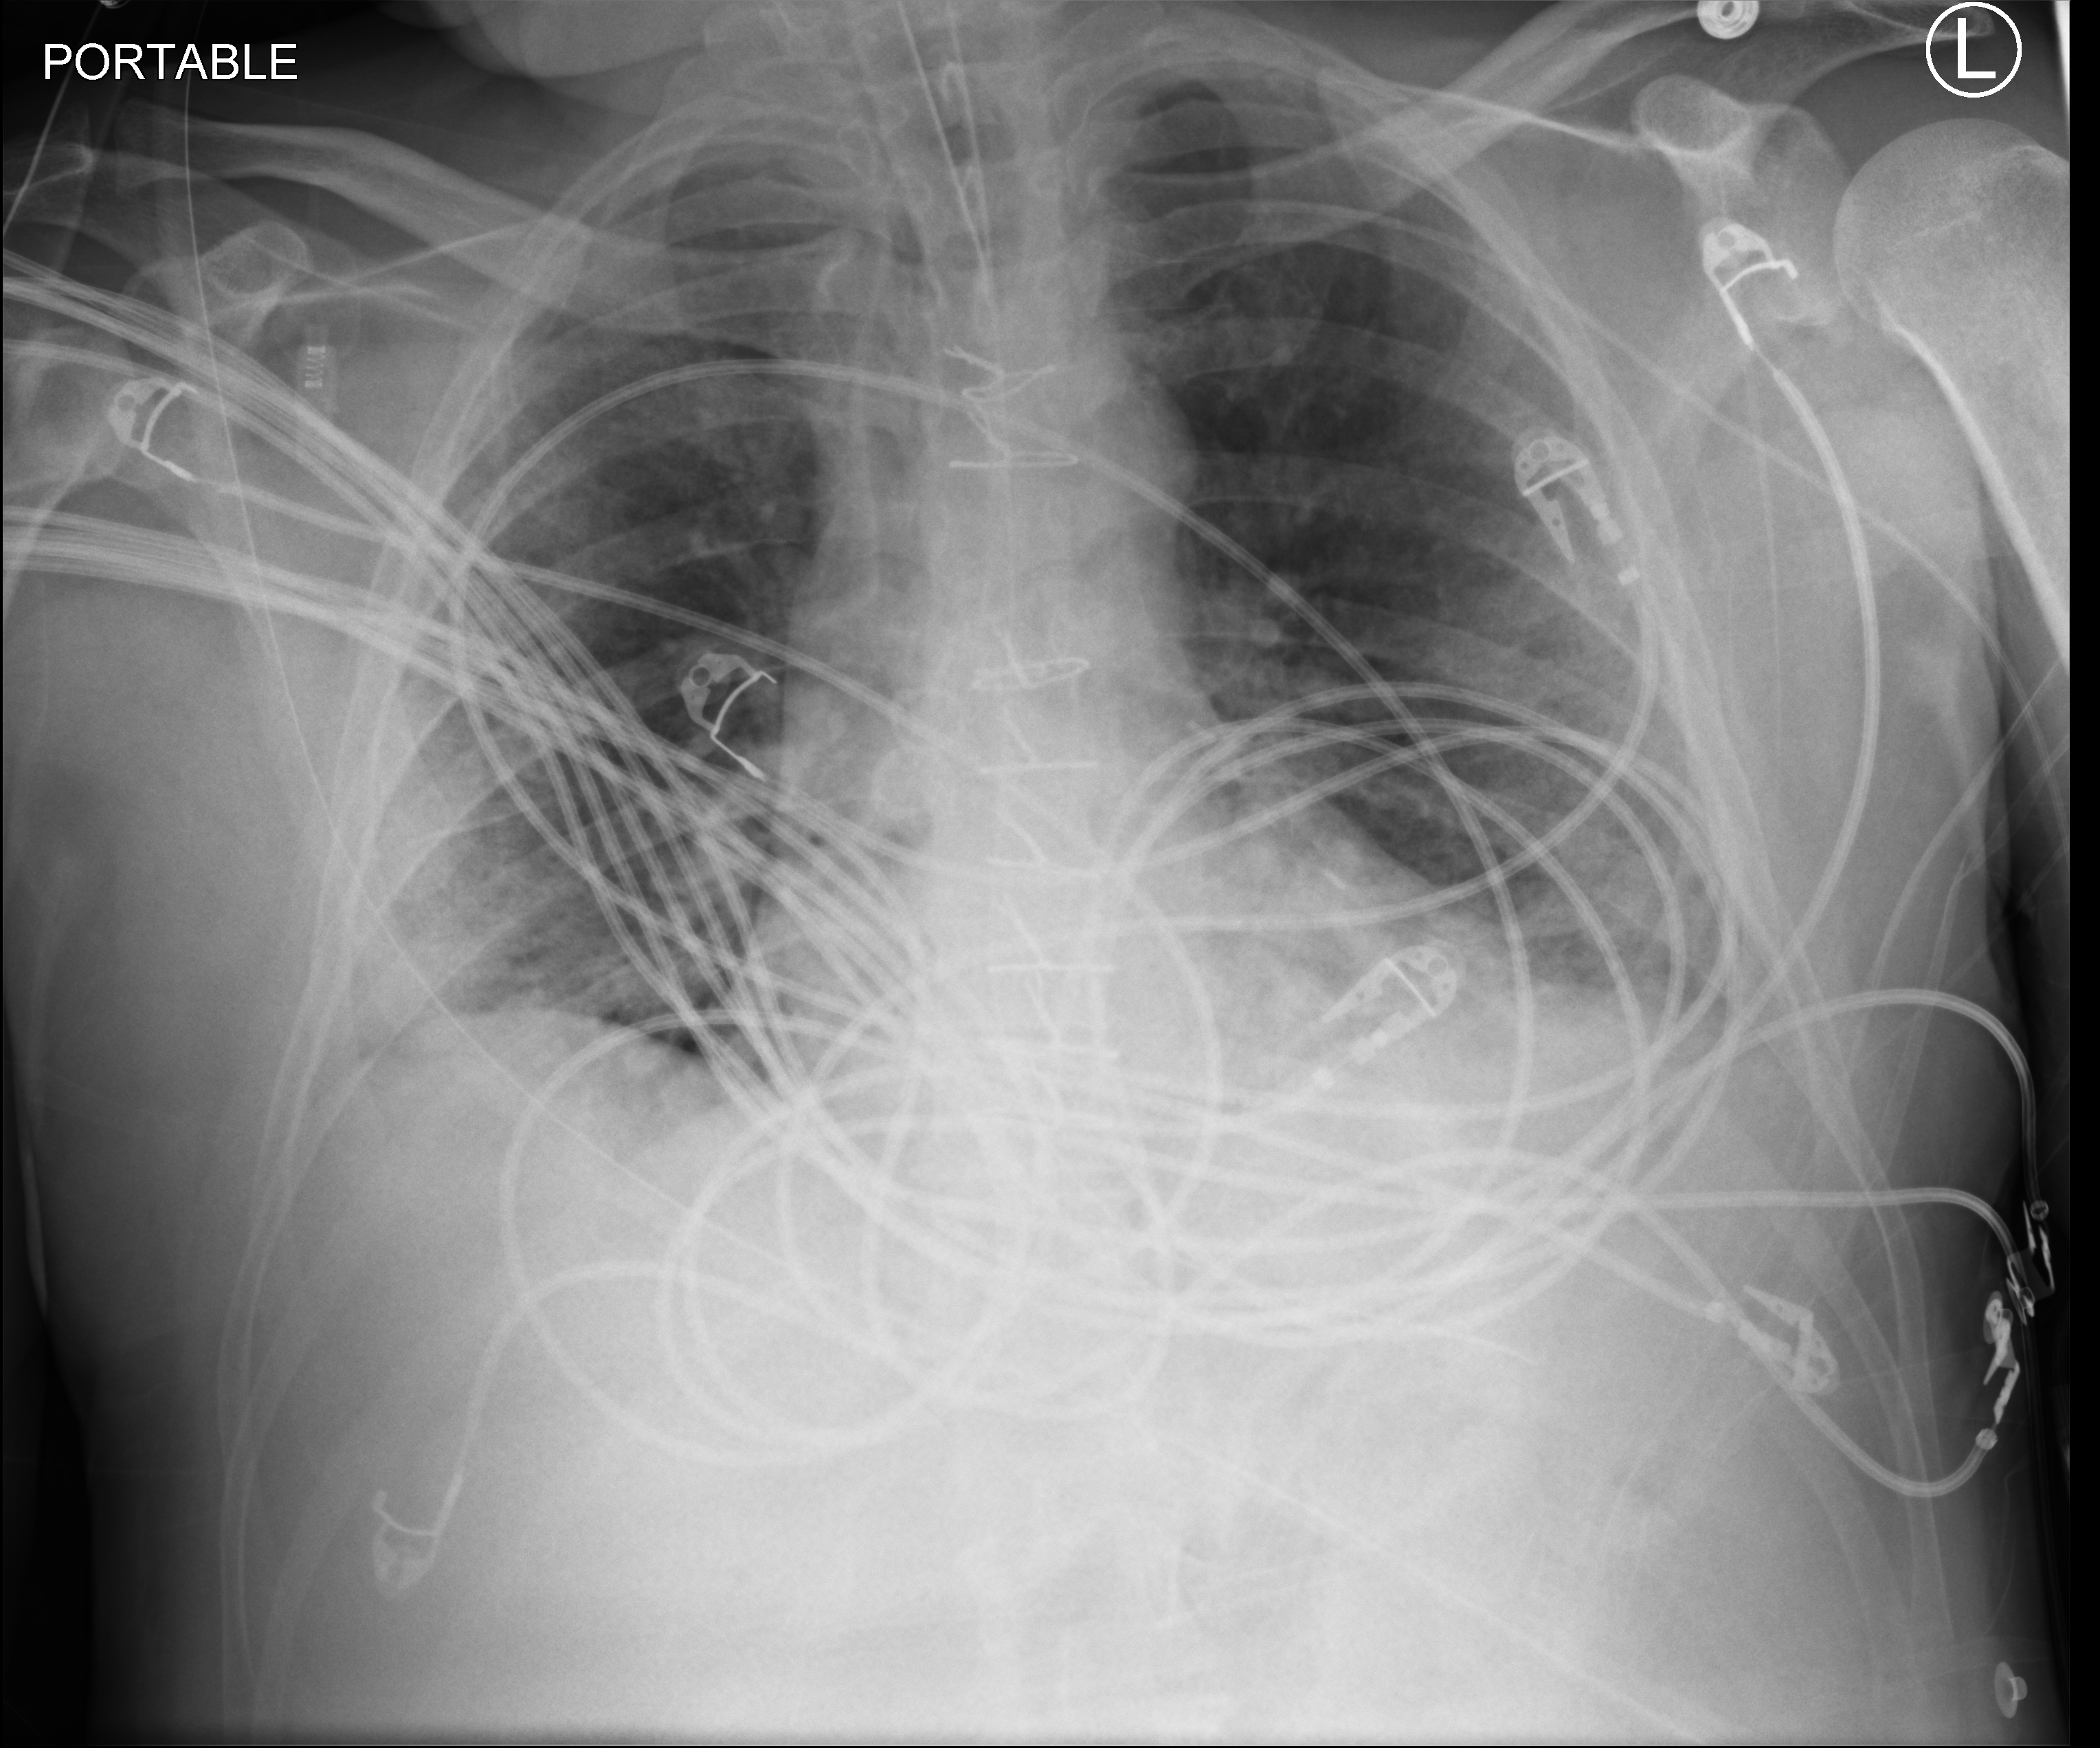
Portable chest radiograph, anteroposterior (AP) projection. Male patient hospitalised with COVID-19, age 18–59 years.
From the hospital-stay record, not from the radiograph (when in the stay this image was taken is not recorded):
- admitted to intensive care during this hospital stay: yes